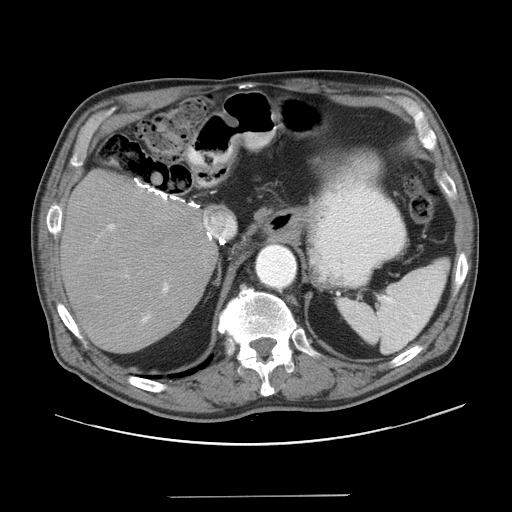
Contrast-enhanced abdominal CT, one axial slice; reconstruction kernel STANDARD; intravenous contrast given; soft-tissue window (W 400 / L 40 HU); 5 mm slice thickness; 512 × 512 image matrix, field of view 420 × 420 mm. Male patient, age 75 years. Case-level facts recorded for this patient, not image findings: diagnosis: colorectal cancer liver metastases, imaged before liver resection; multiple liver metastases: no; largest metastasis: 5.2 cm; disease in both lobes: no.
Annotated regions visible in this slice (expert manual segmentation):
- hepatic veins: bounding box <203,214,236,237> (left, top, right, bottom; pixels)
- liver: <63,172,215,353>
- planned liver remnant (the part of the liver to remain after resection): <66,186,215,353>
- portal vein (with intrahepatic branches): <95,223,169,324>